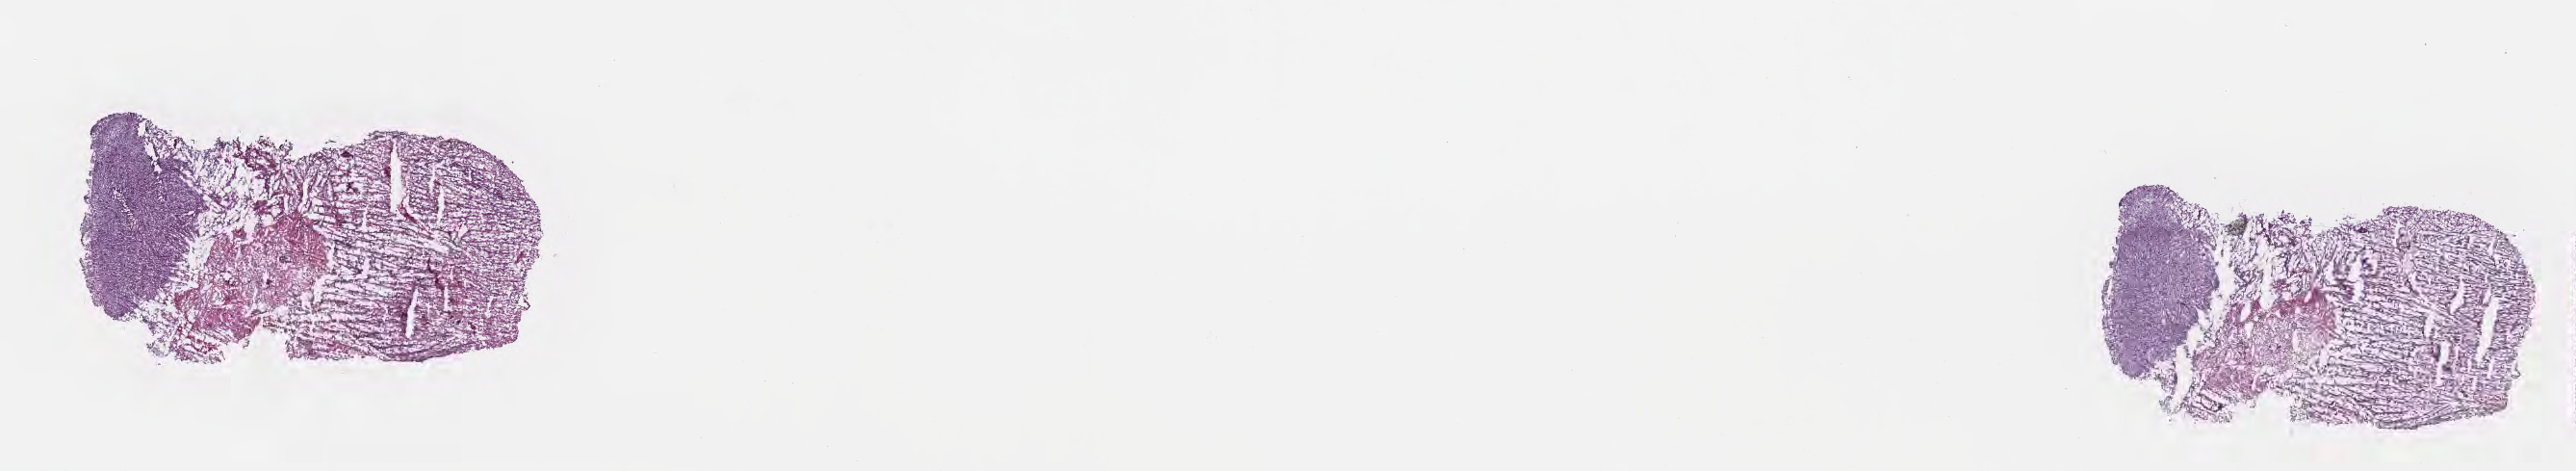
Haematoxylin and eosin whole-slide image, shown as a low-resolution overview of the whole scanned area (about 21.6 x 4.0 mm). Frozen section. Specimen: primary tumor. Anatomic site: brain. Male, age 45 years at initial diagnosis. Pathologist review of this section (percent, as recorded): tumor cells 37%, tumor nuclei 82%.
Histologic diagnosis: Glioblastoma, NOS.